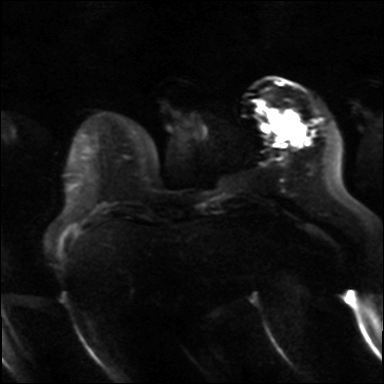
Breast MRI, one axial slice. Slice 8 of 36 in the series (ordered by position). Diffusion-weighted series; image 2 of 4 stored at this slice position (different b-values; order by instance number). 3 T. 384 × 384 image matrix. Female patient.
Annotated regions visible in this slice (outlined manually by an expert reader):
- tumour on diffusion-weighted imaging: bounding box <299,126,303,135> (left, top, right, bottom; pixels)